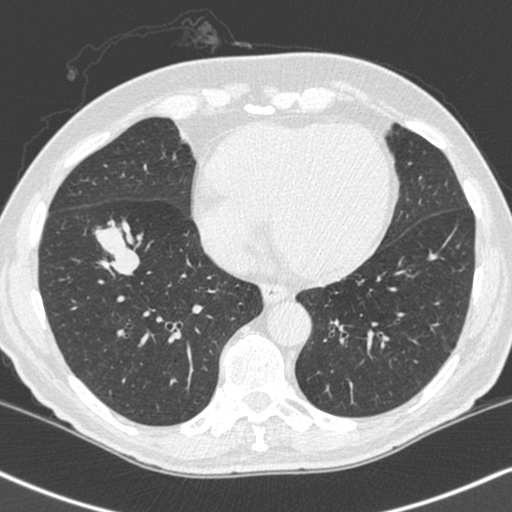
Chest CT (low-dose screening protocol), one axial image. First (baseline) screen. Lung window (W 1500 / L -600 HU). Slice 155 of 248 in the series. 512 × 512 image matrix. Male, age 68 years at enrolment. Current smoker at enrolment.
Lesion marked by an expert reader, bounding box [x1, y1, x2, y2] px = [80, 209, 155, 279]. The exam's reader record, not a measurement of the box and not confirmed to be the same lesion: non-calcified nodule or mass ≥4 mm, right lower lobe, 34 × 17 mm, smooth margins, soft tissue attenuation. Lung cancer was diagnosed 24 days after this screen: combined small cell carcinoma, right lower lobe, stage IIIA (AJCC 6th edition), 41 mm at pathology.